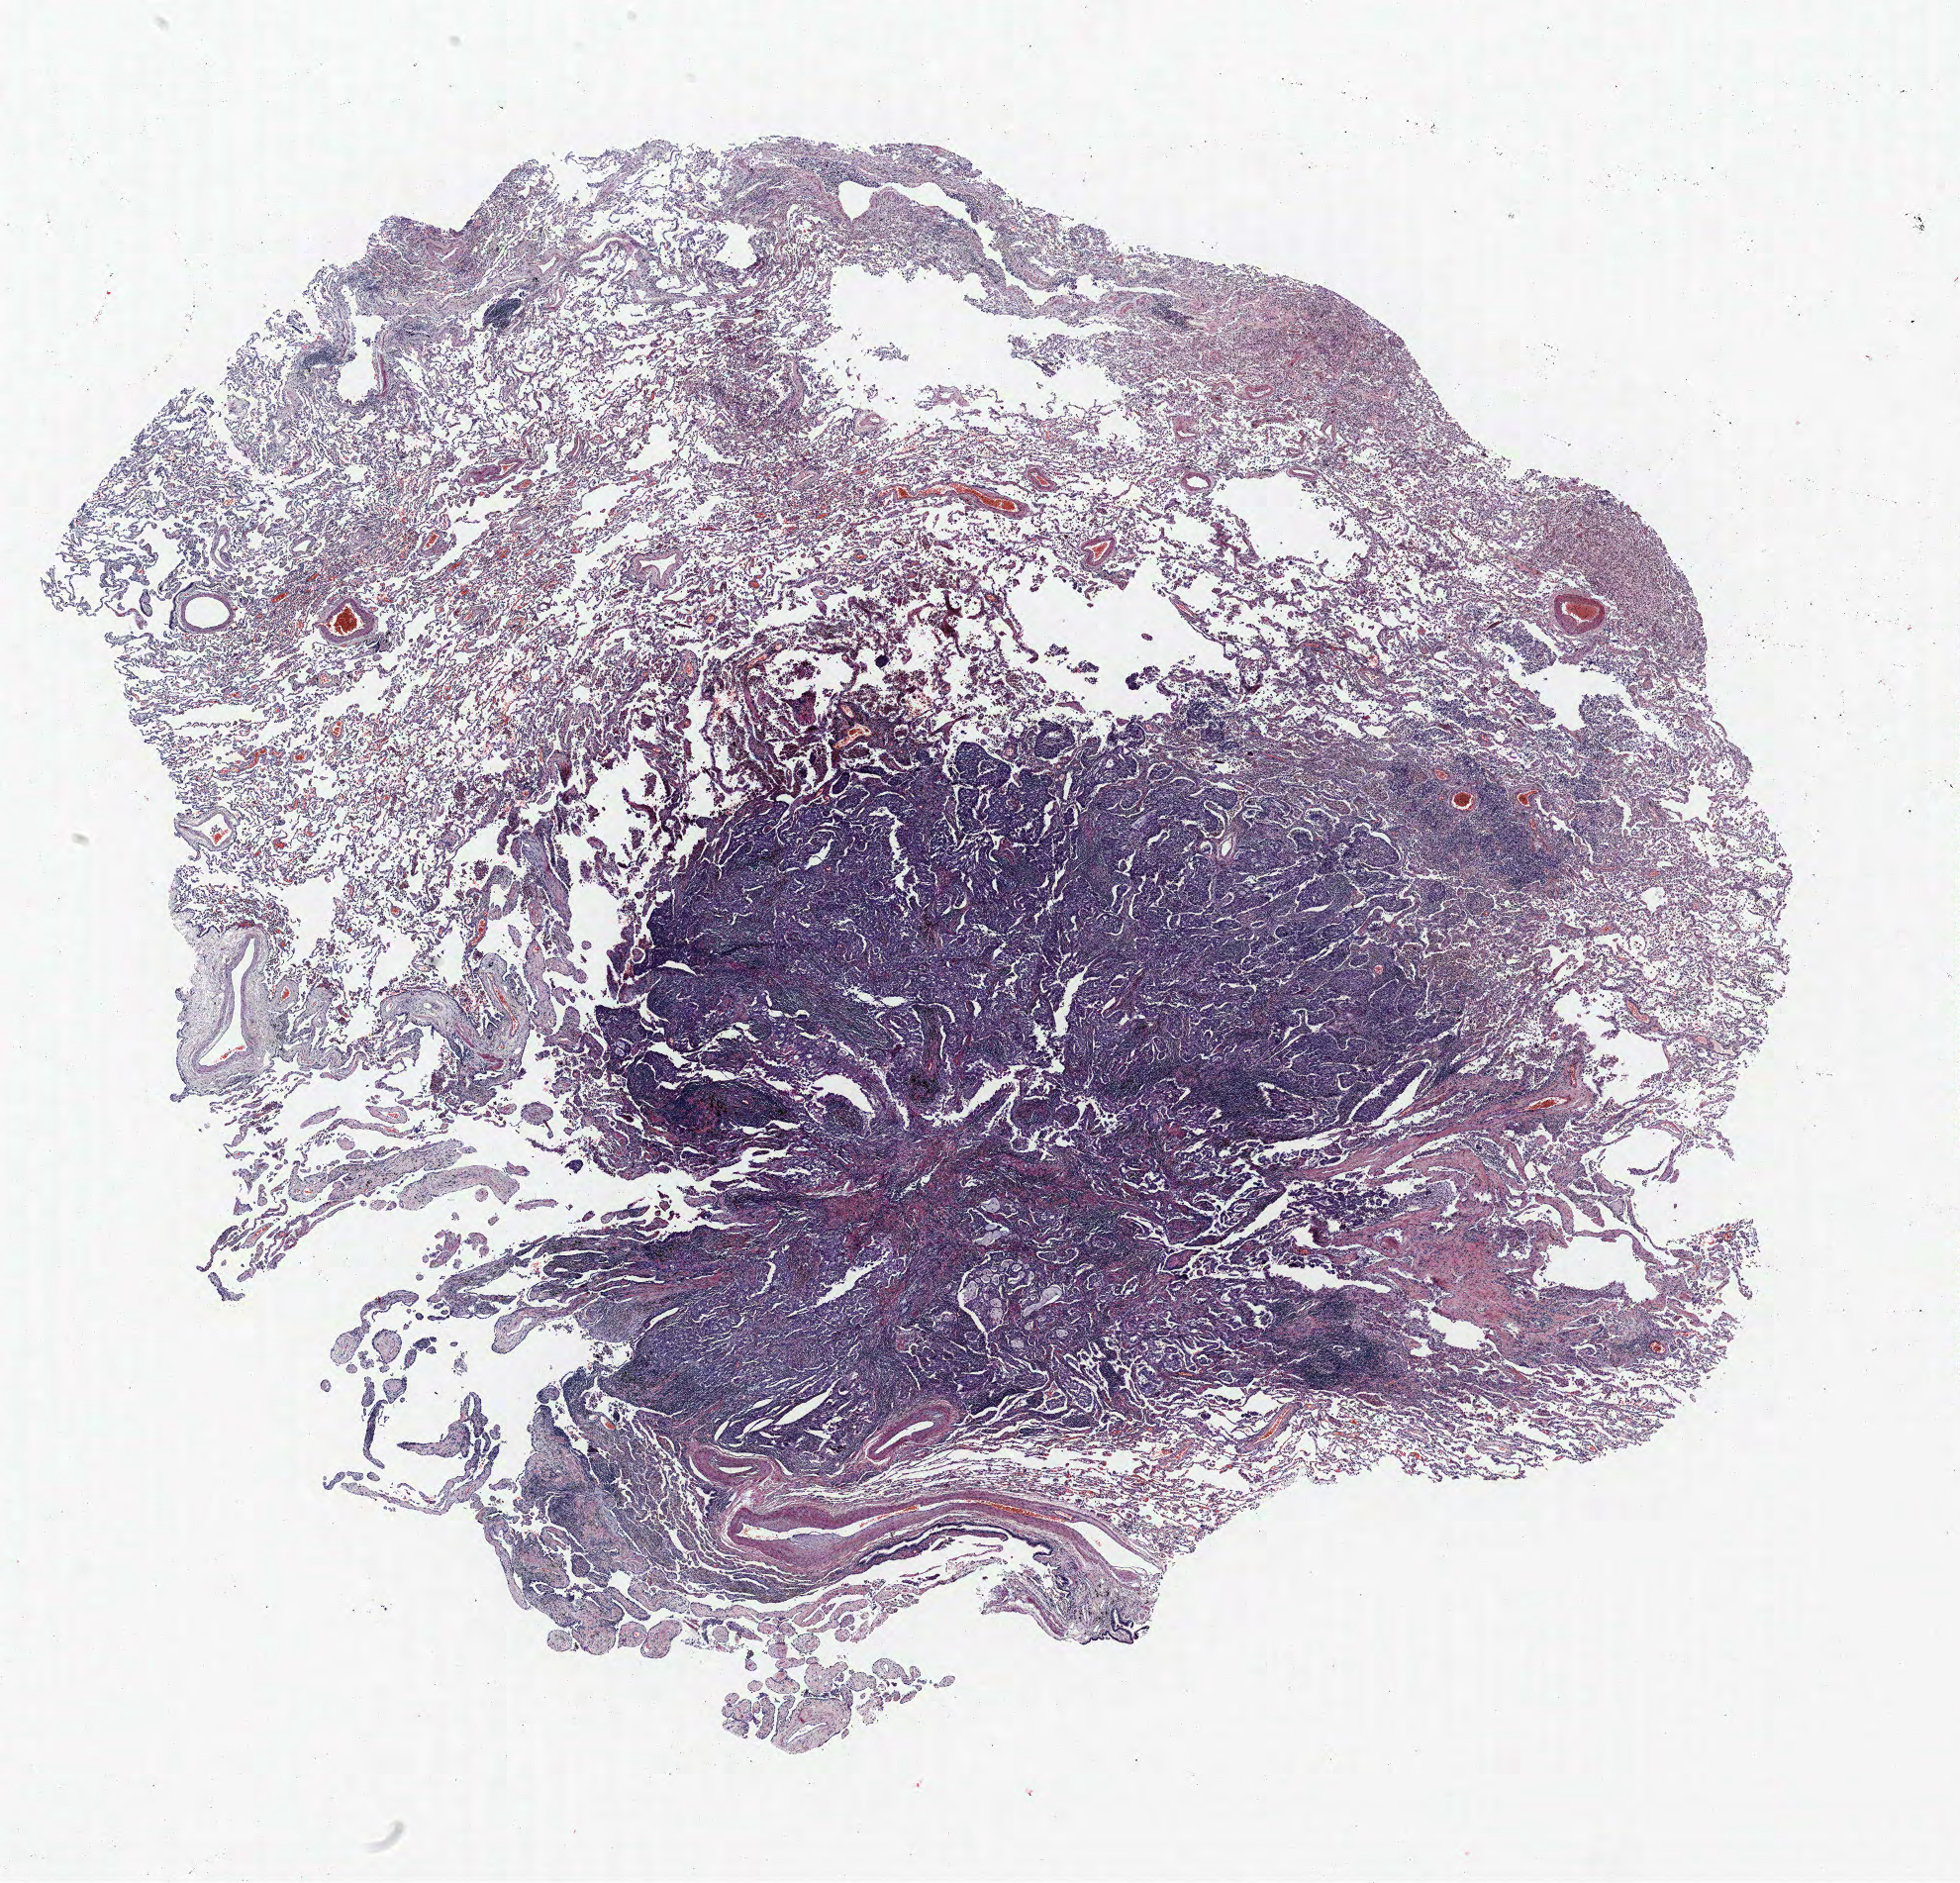
Whole-slide histology image, Hematoxylin and eosin (H&E) stained, a low-resolution overview of the entire scanned area, about 15.8 x 15.2 mm. Formalin-fixed paraffin-embedded (FFPE) section. Lung. Male patient, aged 58 at enrolment. Current smoker at enrolment.
Stage (AJCC 6th edition): IA. Tumour size (pathology): 9 mm. Participant's lung-cancer diagnosis: Adenocarcinoma, NOS. Primary tumour location (clinical record): left upper lobe.